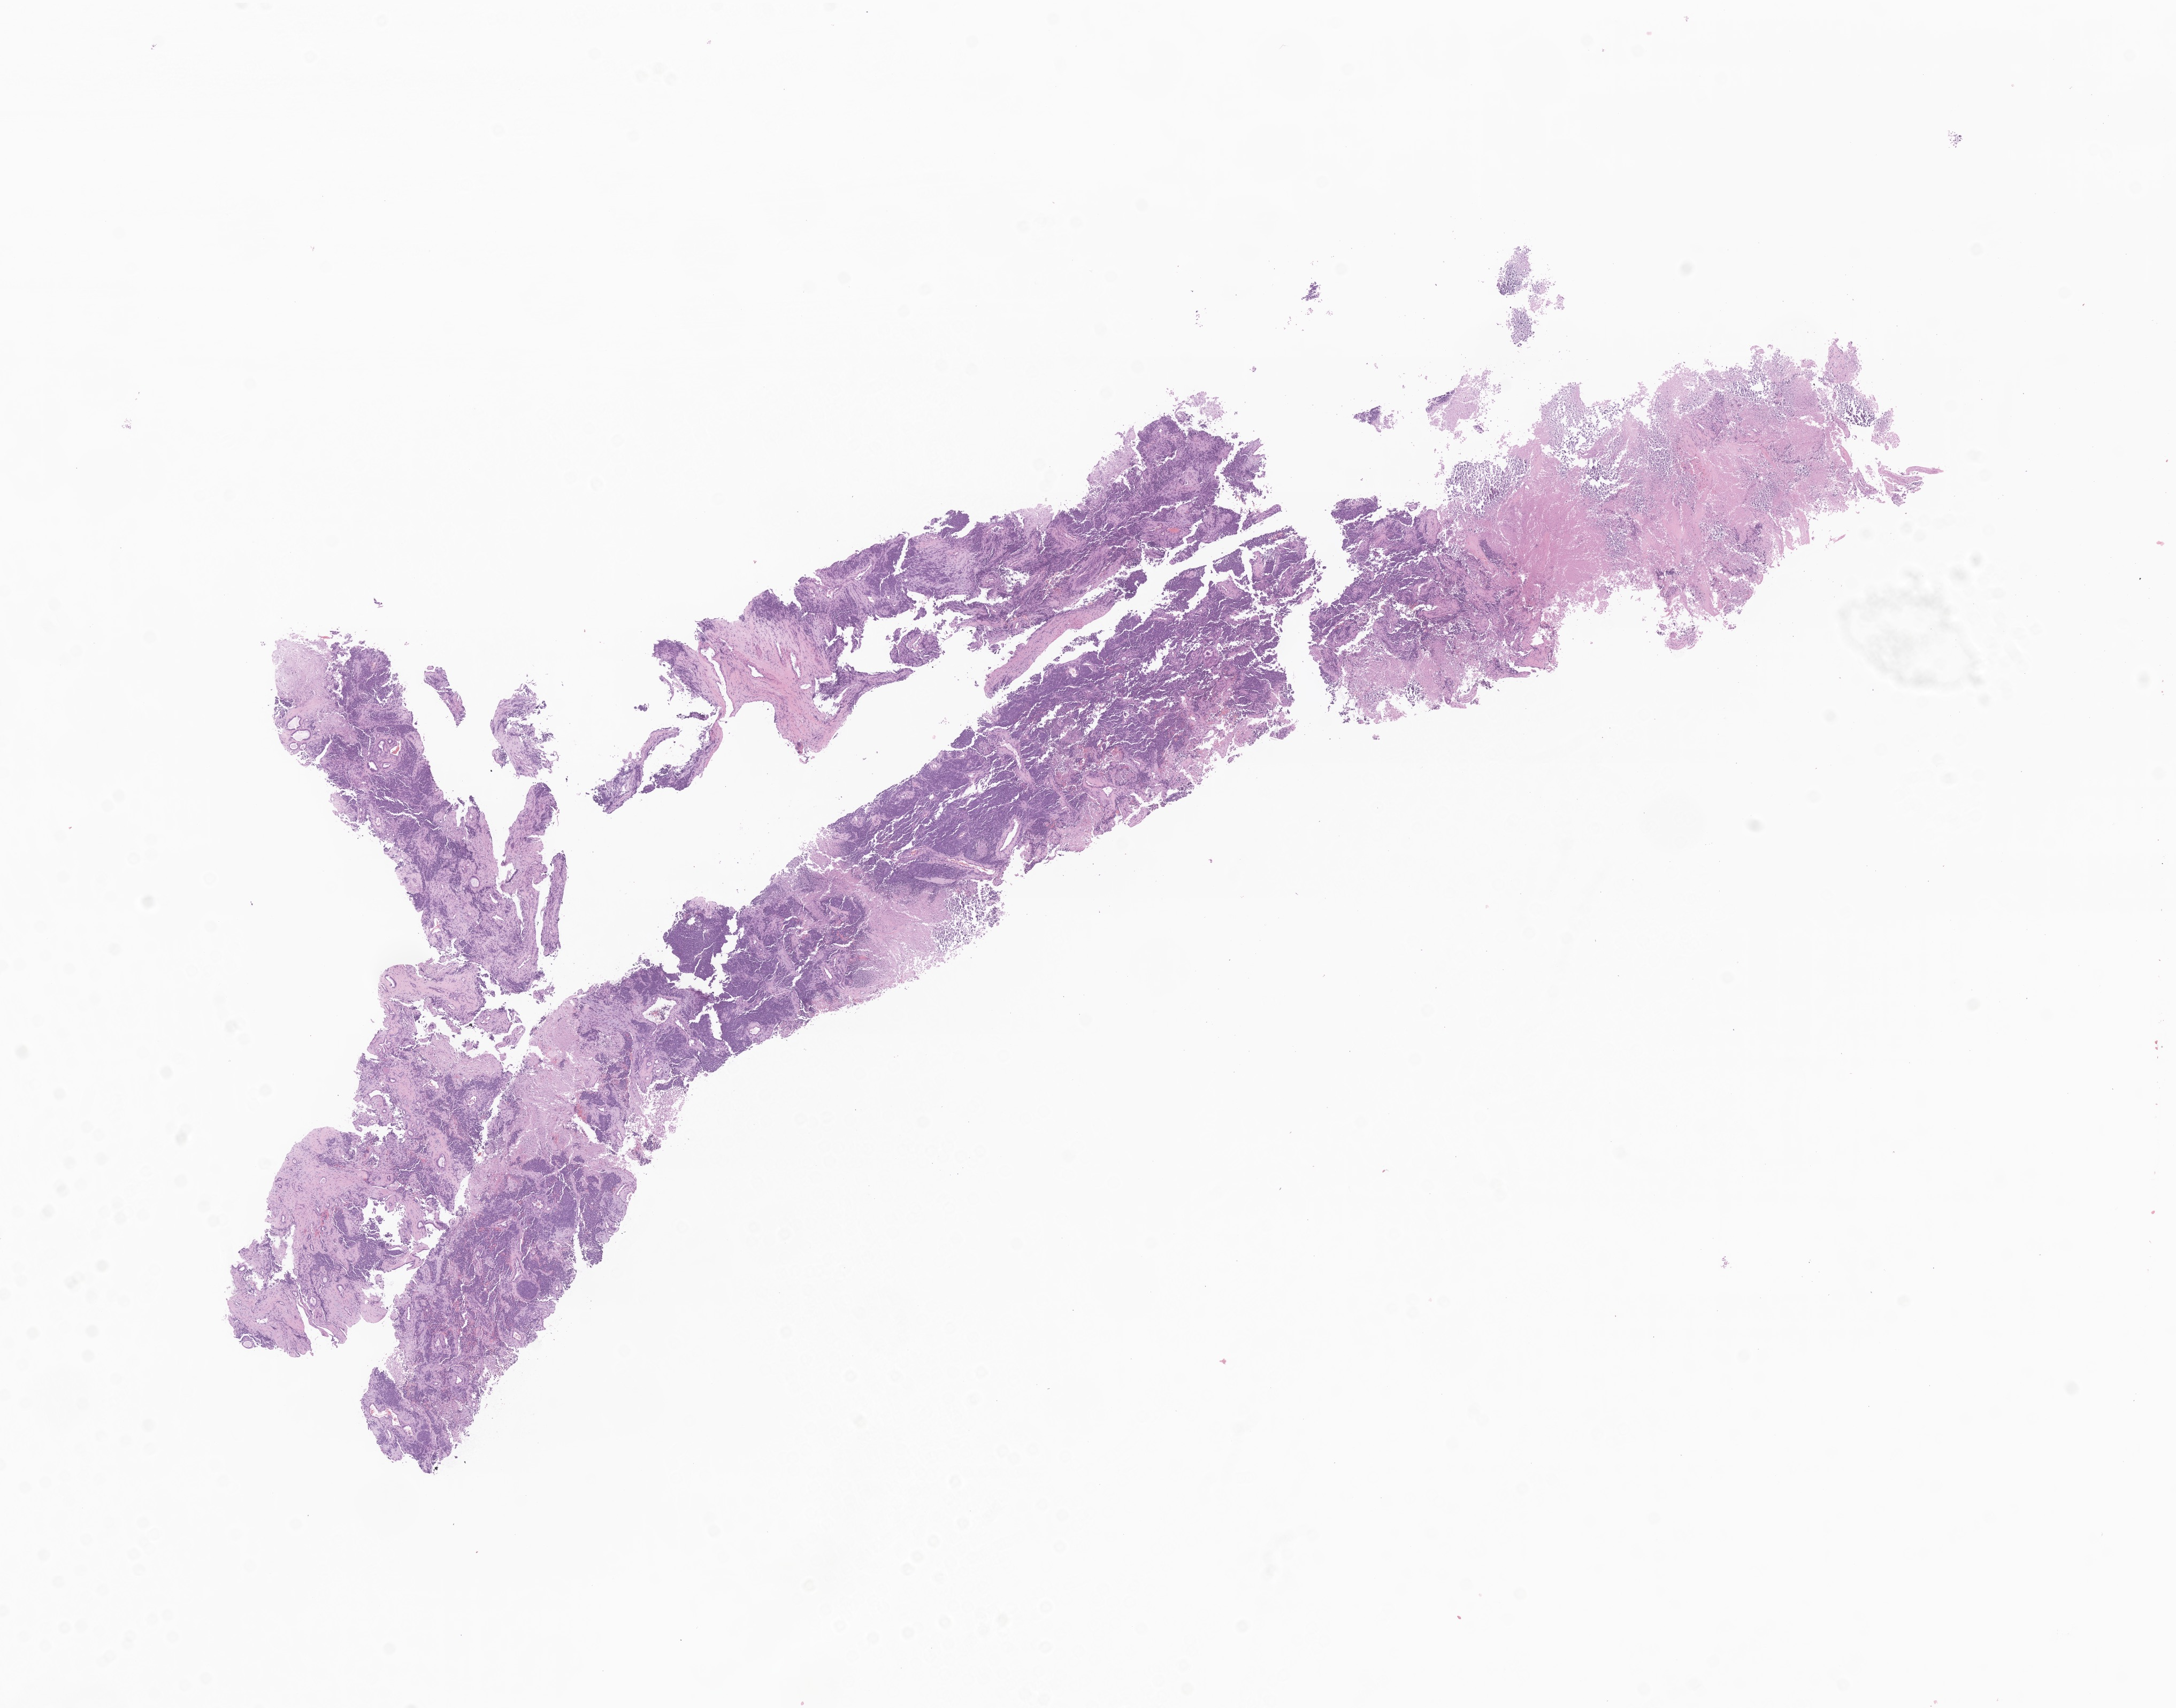
Digitized hematoxylin and eosin (H&E)-stained section of tumor tissue from the kidney, a low-resolution overview of the entire scanned area, about 17.1 x 13.5 mm; FFPE section. Patient female; age 132 months (11 years).
Diagnosis (ICD-O-3 morphology term): Ewing sarcoma.